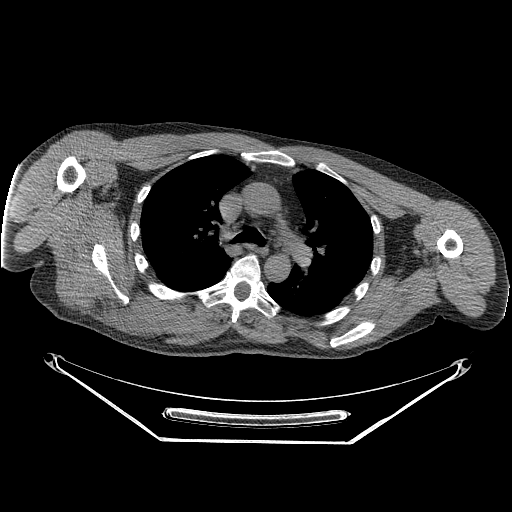
CT of an extremity soft-tissue mass (from a PET/CT study), one axial slice. Position 183 of 267 along the scan axis. 140 kVp. Soft-tissue window (W 400 / L 40 HU). 512 × 512 image matrix, field of view 500 × 500 mm. Male patient. From the clinical record (not read from this slice): histological type: pleiomorphic spindle cell undifferentiated; grade: high; site of the primary tumour: right parascapusular.
Structures marked on this image (expert contour drawn on MRI and transferred to this co-registered scan by the dataset authors):
- gross tumour volume including surrounding oedema: bounding box [x1, y1, x2, y2] px = [85, 285, 215, 337]
- gross tumour volume (mass): [100, 288, 172, 330]